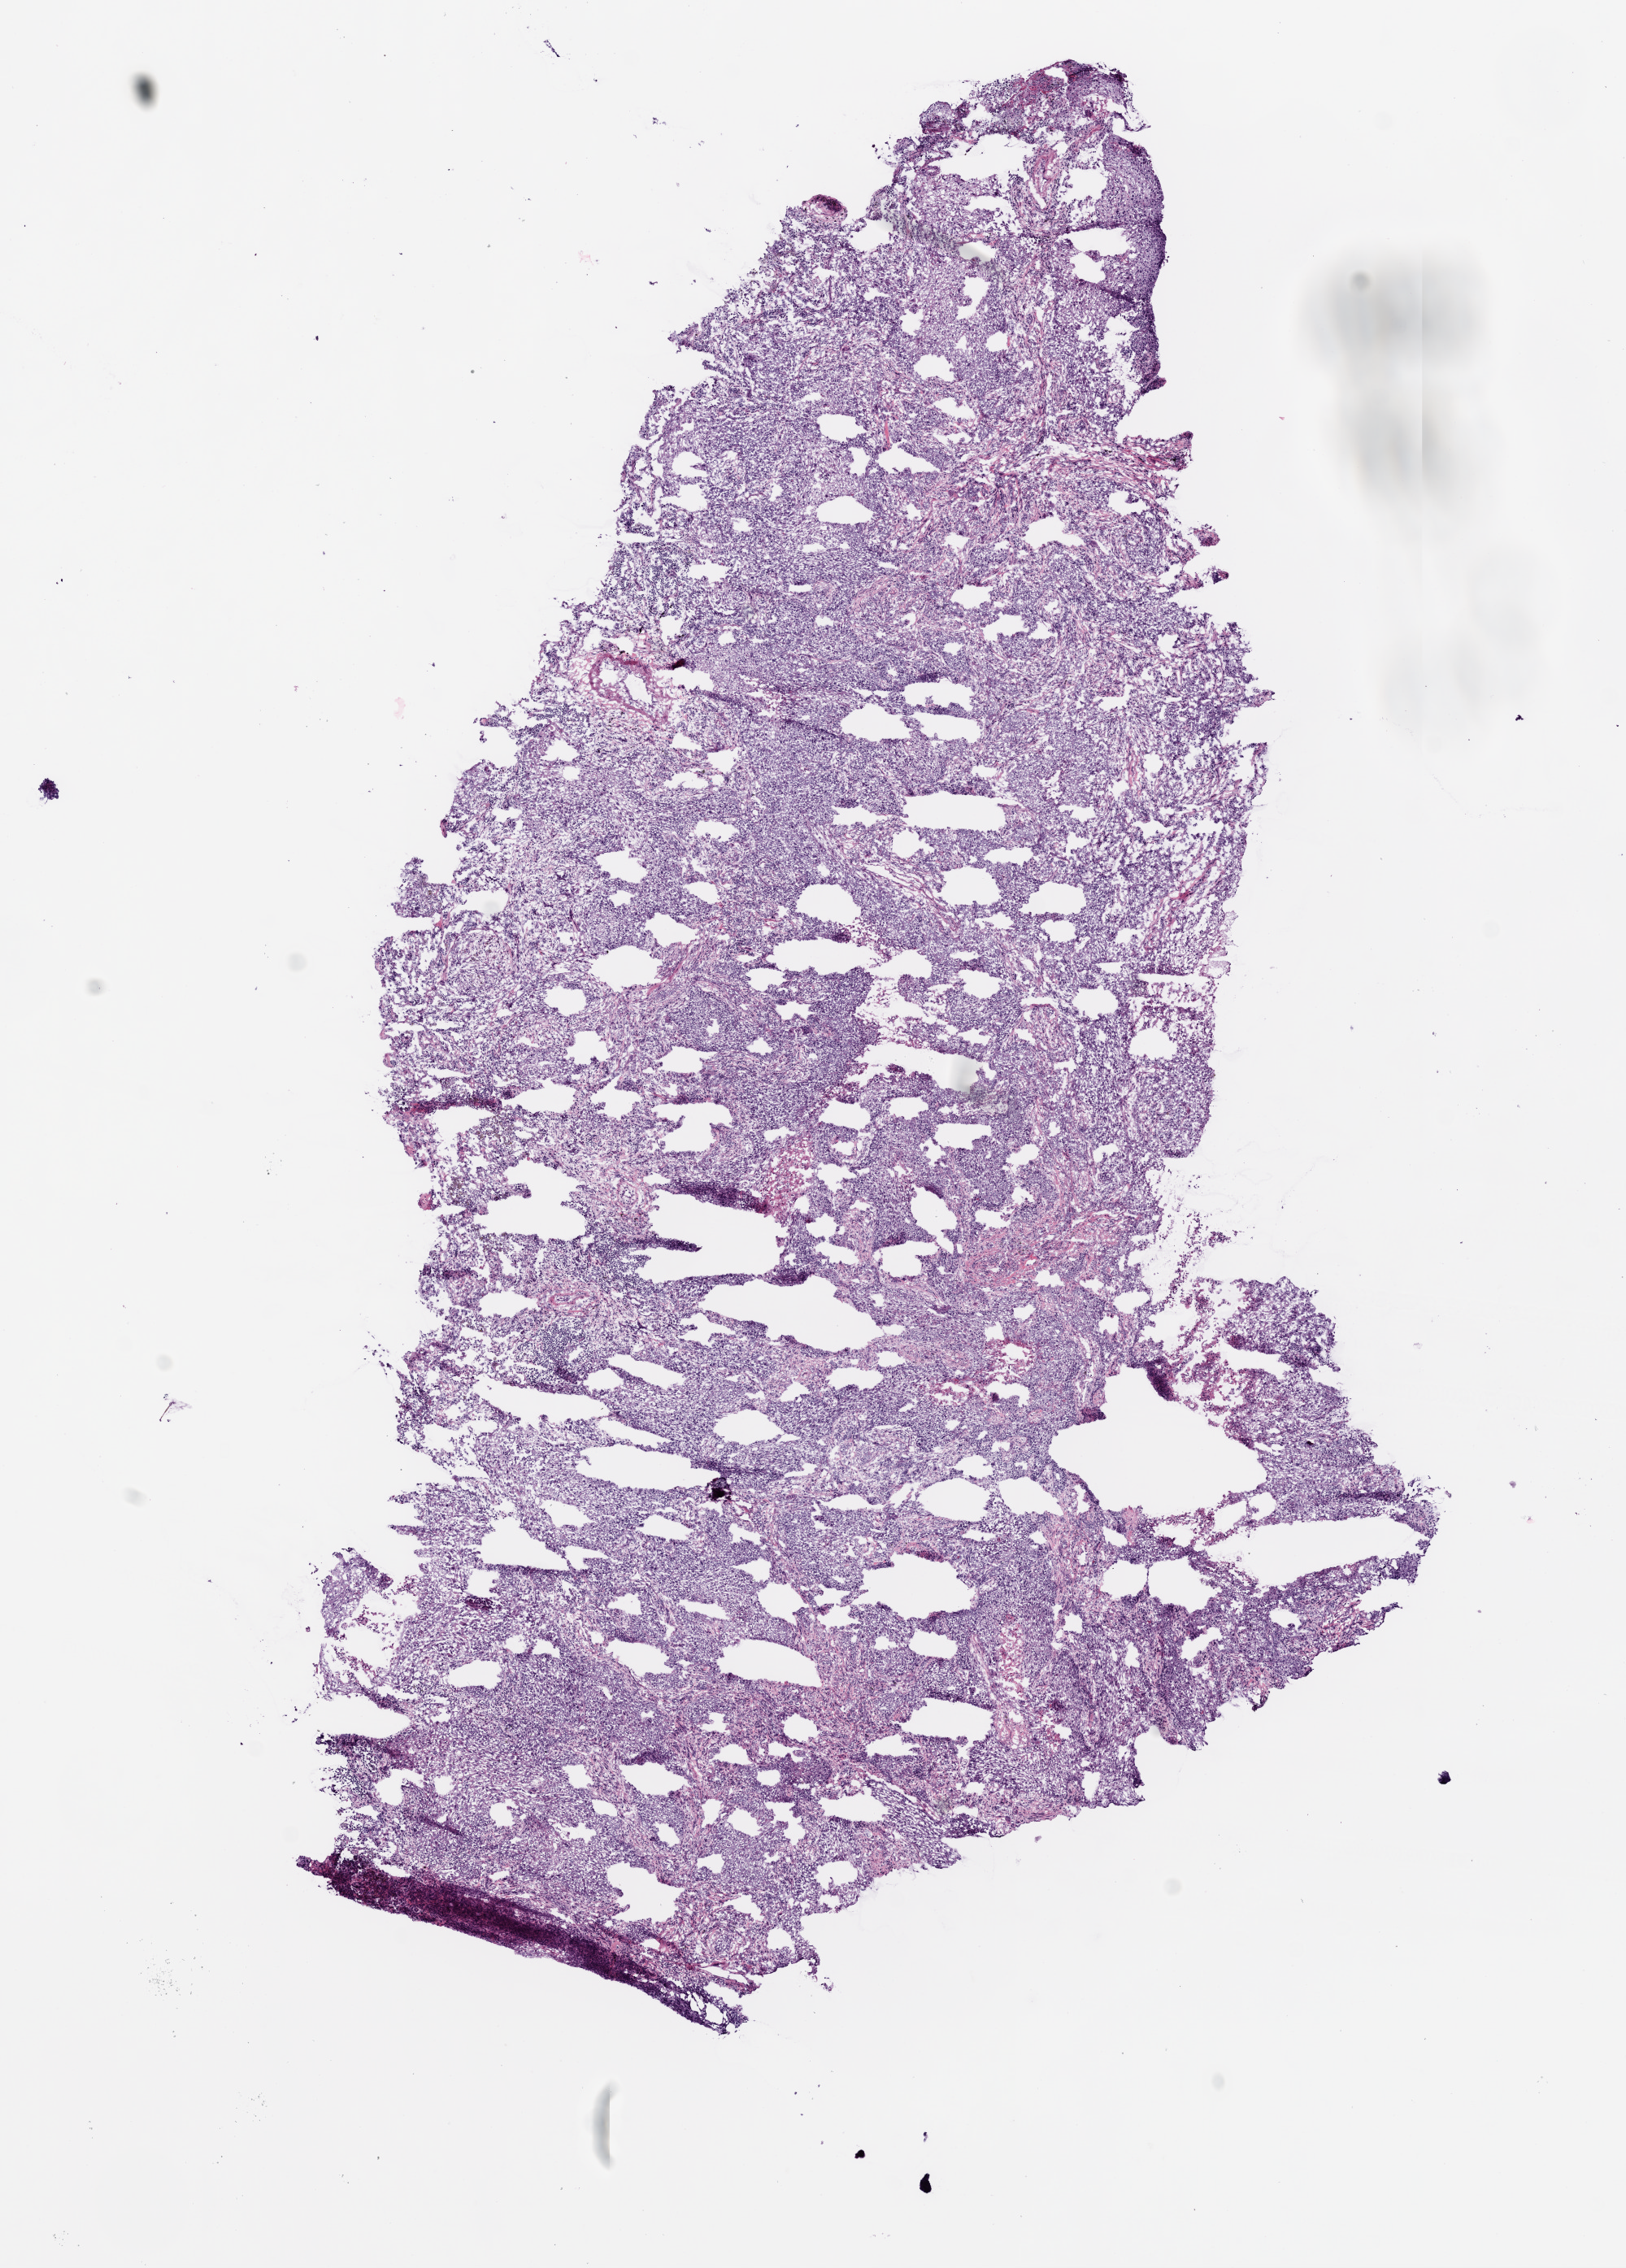
Hematoxylin and eosin (H&E) stained whole-slide image, low-resolution overview of the scanned area, about 8.0 x 11.2 mm; frozen section; lung, primary tumour sample. Male, age 64 years at initial diagnosis. Pathologist review of this section (percent, as recorded): tumour cells 75%, tumour nuclei 80%, normal cells 15%, stromal cells 5%, necrosis 5%.
- histologic diagnosis: Squamous cell carcinoma, NOS (lower lobe, lung)
- AJCC pathologic stage: IB